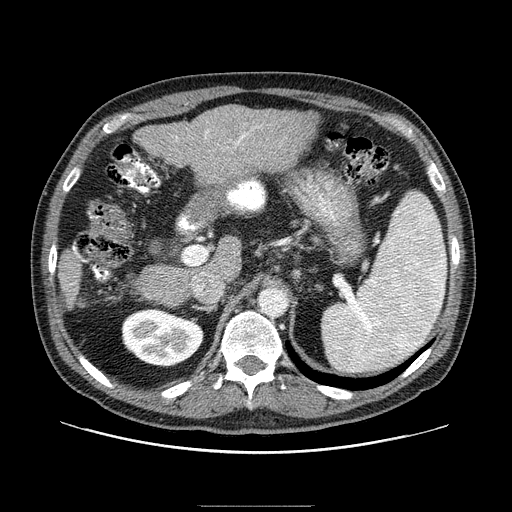
Contrast-enhanced abdominal CT (liver protocol), one axial slice. Slice 48 of 99 in the series (ordered by position). 100 kVp. One of 2 acquisitions stored at this slice position. Soft-tissue window (W 400 / L 40 HU). 512 × 512 image matrix. Case-level facts recorded for this patient, not image findings: diagnosis: hepatocellular carcinoma (patient treated with transarterial chemoembolisation; whether this scan precedes or follows treatment is not stated here); TNM stage (as recorded): Stage-II; Child-Pugh class: A; tumour differentiation: well differentiated.
Structures marked on this image (semi-automatically segmented with operator editing):
- liver parenchyma outside the tumour (the mass and vessels are separate outlines, so this box may not span the whole liver): bounding box (x1, y1, x2, y2) in pixels: (58, 105, 318, 310)
- liver vessels: (176, 130, 249, 146)